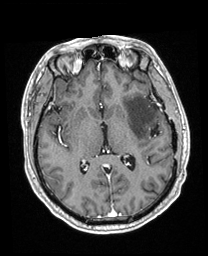
Brain MRI from a brain-tumour surgery series, one axial slice; slice 107 of 208 in the series (ordered by position); T1-weighted post-contrast; 208 × 256 image matrix, field of view 211 × 260 mm. Case-level facts recorded for this patient, not image findings: histopathology: Astrocytoma; WHO grade: 3; IDH mutation: yes.
Annotated regions visible in this slice (expert manual segmentation):
- previous resection cavity: bounding box [x1, y1, x2, y2] px = [151, 124, 160, 137]